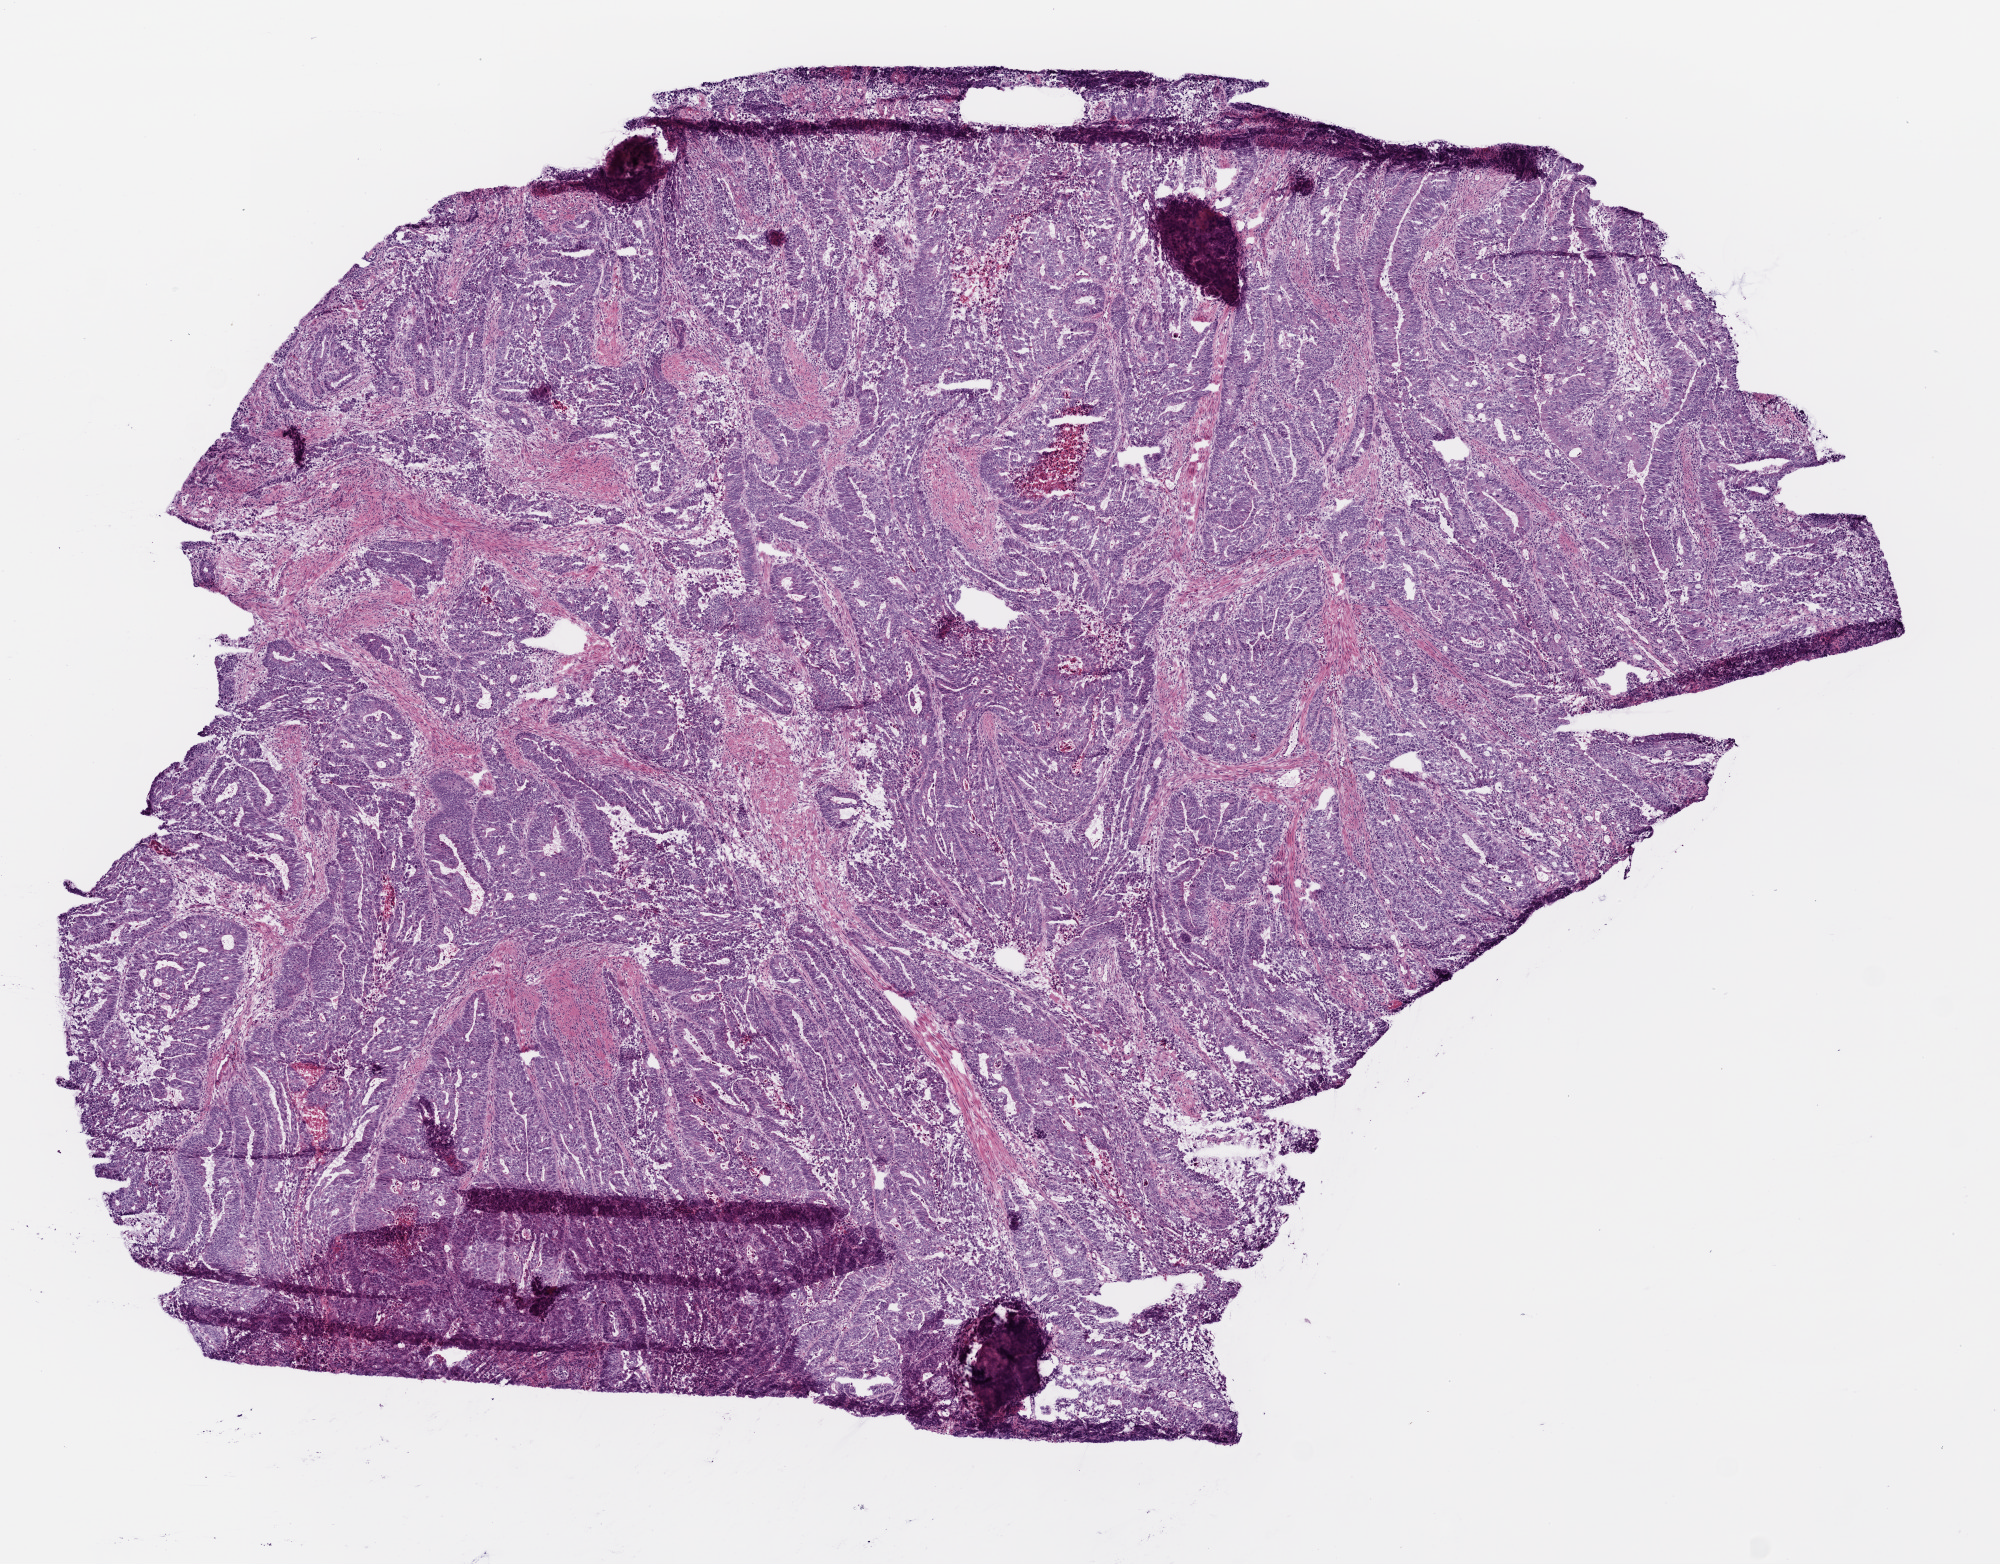
Whole-slide histology image, Hematoxylin and eosin (H&E) stained, a low-resolution overview of the entire scanned area, about 8.0 x 6.3 mm (slide scanned at 20x). Frozen section from the top of the tissue portion. Colon, primary tumour sample. Patient: male, age at initial diagnosis 70 years. Composition of this section per pathologist review: tumour cells 80%, tumour nuclei 90%, normal cells 0%, stromal cells 20%, necrosis 0%.
Pathologic diagnosis: Adenocarcinoma, NOS (rectosigmoid junction). TNM: T2 N1 M0. AJCC pathologic stage: IIIA. Lymph nodes positive (case pathology): 2 of 16 examined.